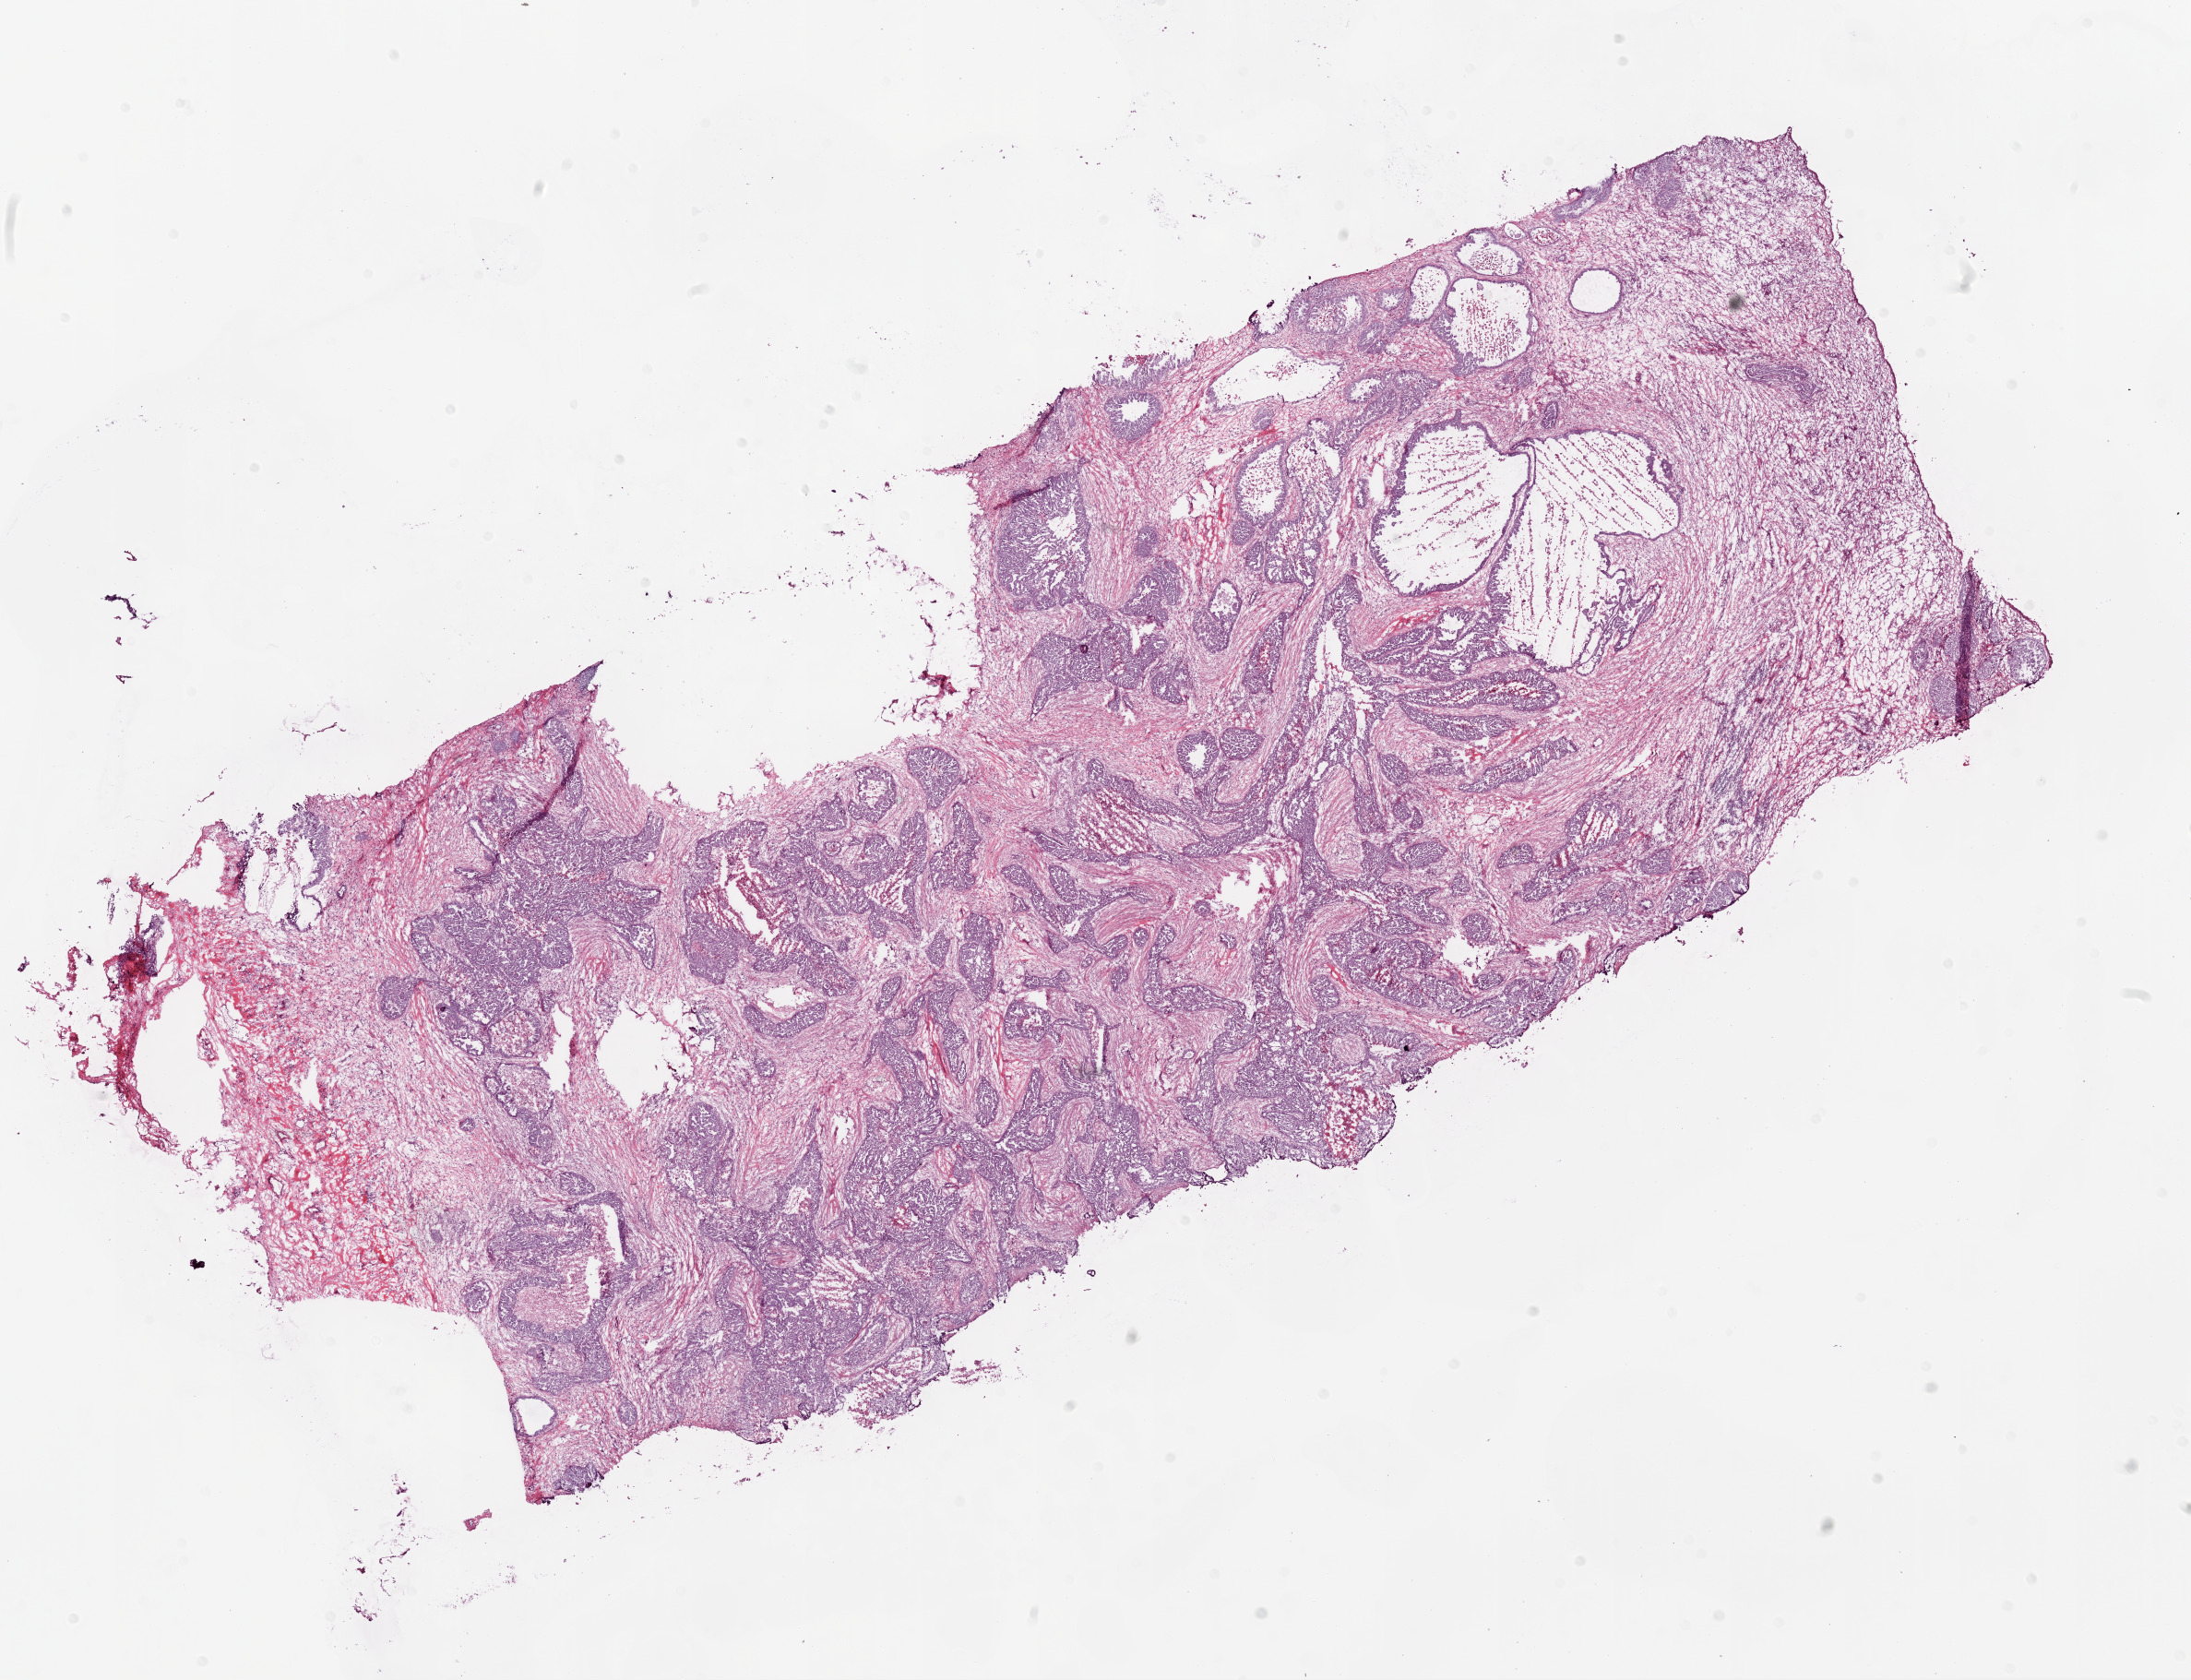
Whole-slide histology image, H&E, shown as a low-resolution overview of the whole scanned area (about 19.1 x 14.6 mm), frozen section from the bottom of the tissue portion, primary tumour sample from the ovary. Female, age 74 years at initial diagnosis. Histologic grade: G2 (moderately differentiated). Pathologist review of this section (percent, as recorded): tumour cells 40%, tumour nuclei 90%, normal cells 0%, stromal cells 50%, necrosis 10%.
Pathologic diagnosis: Serous cystadenocarcinoma, NOS (peritoneum, NOS). FIGO stage: IIIC.